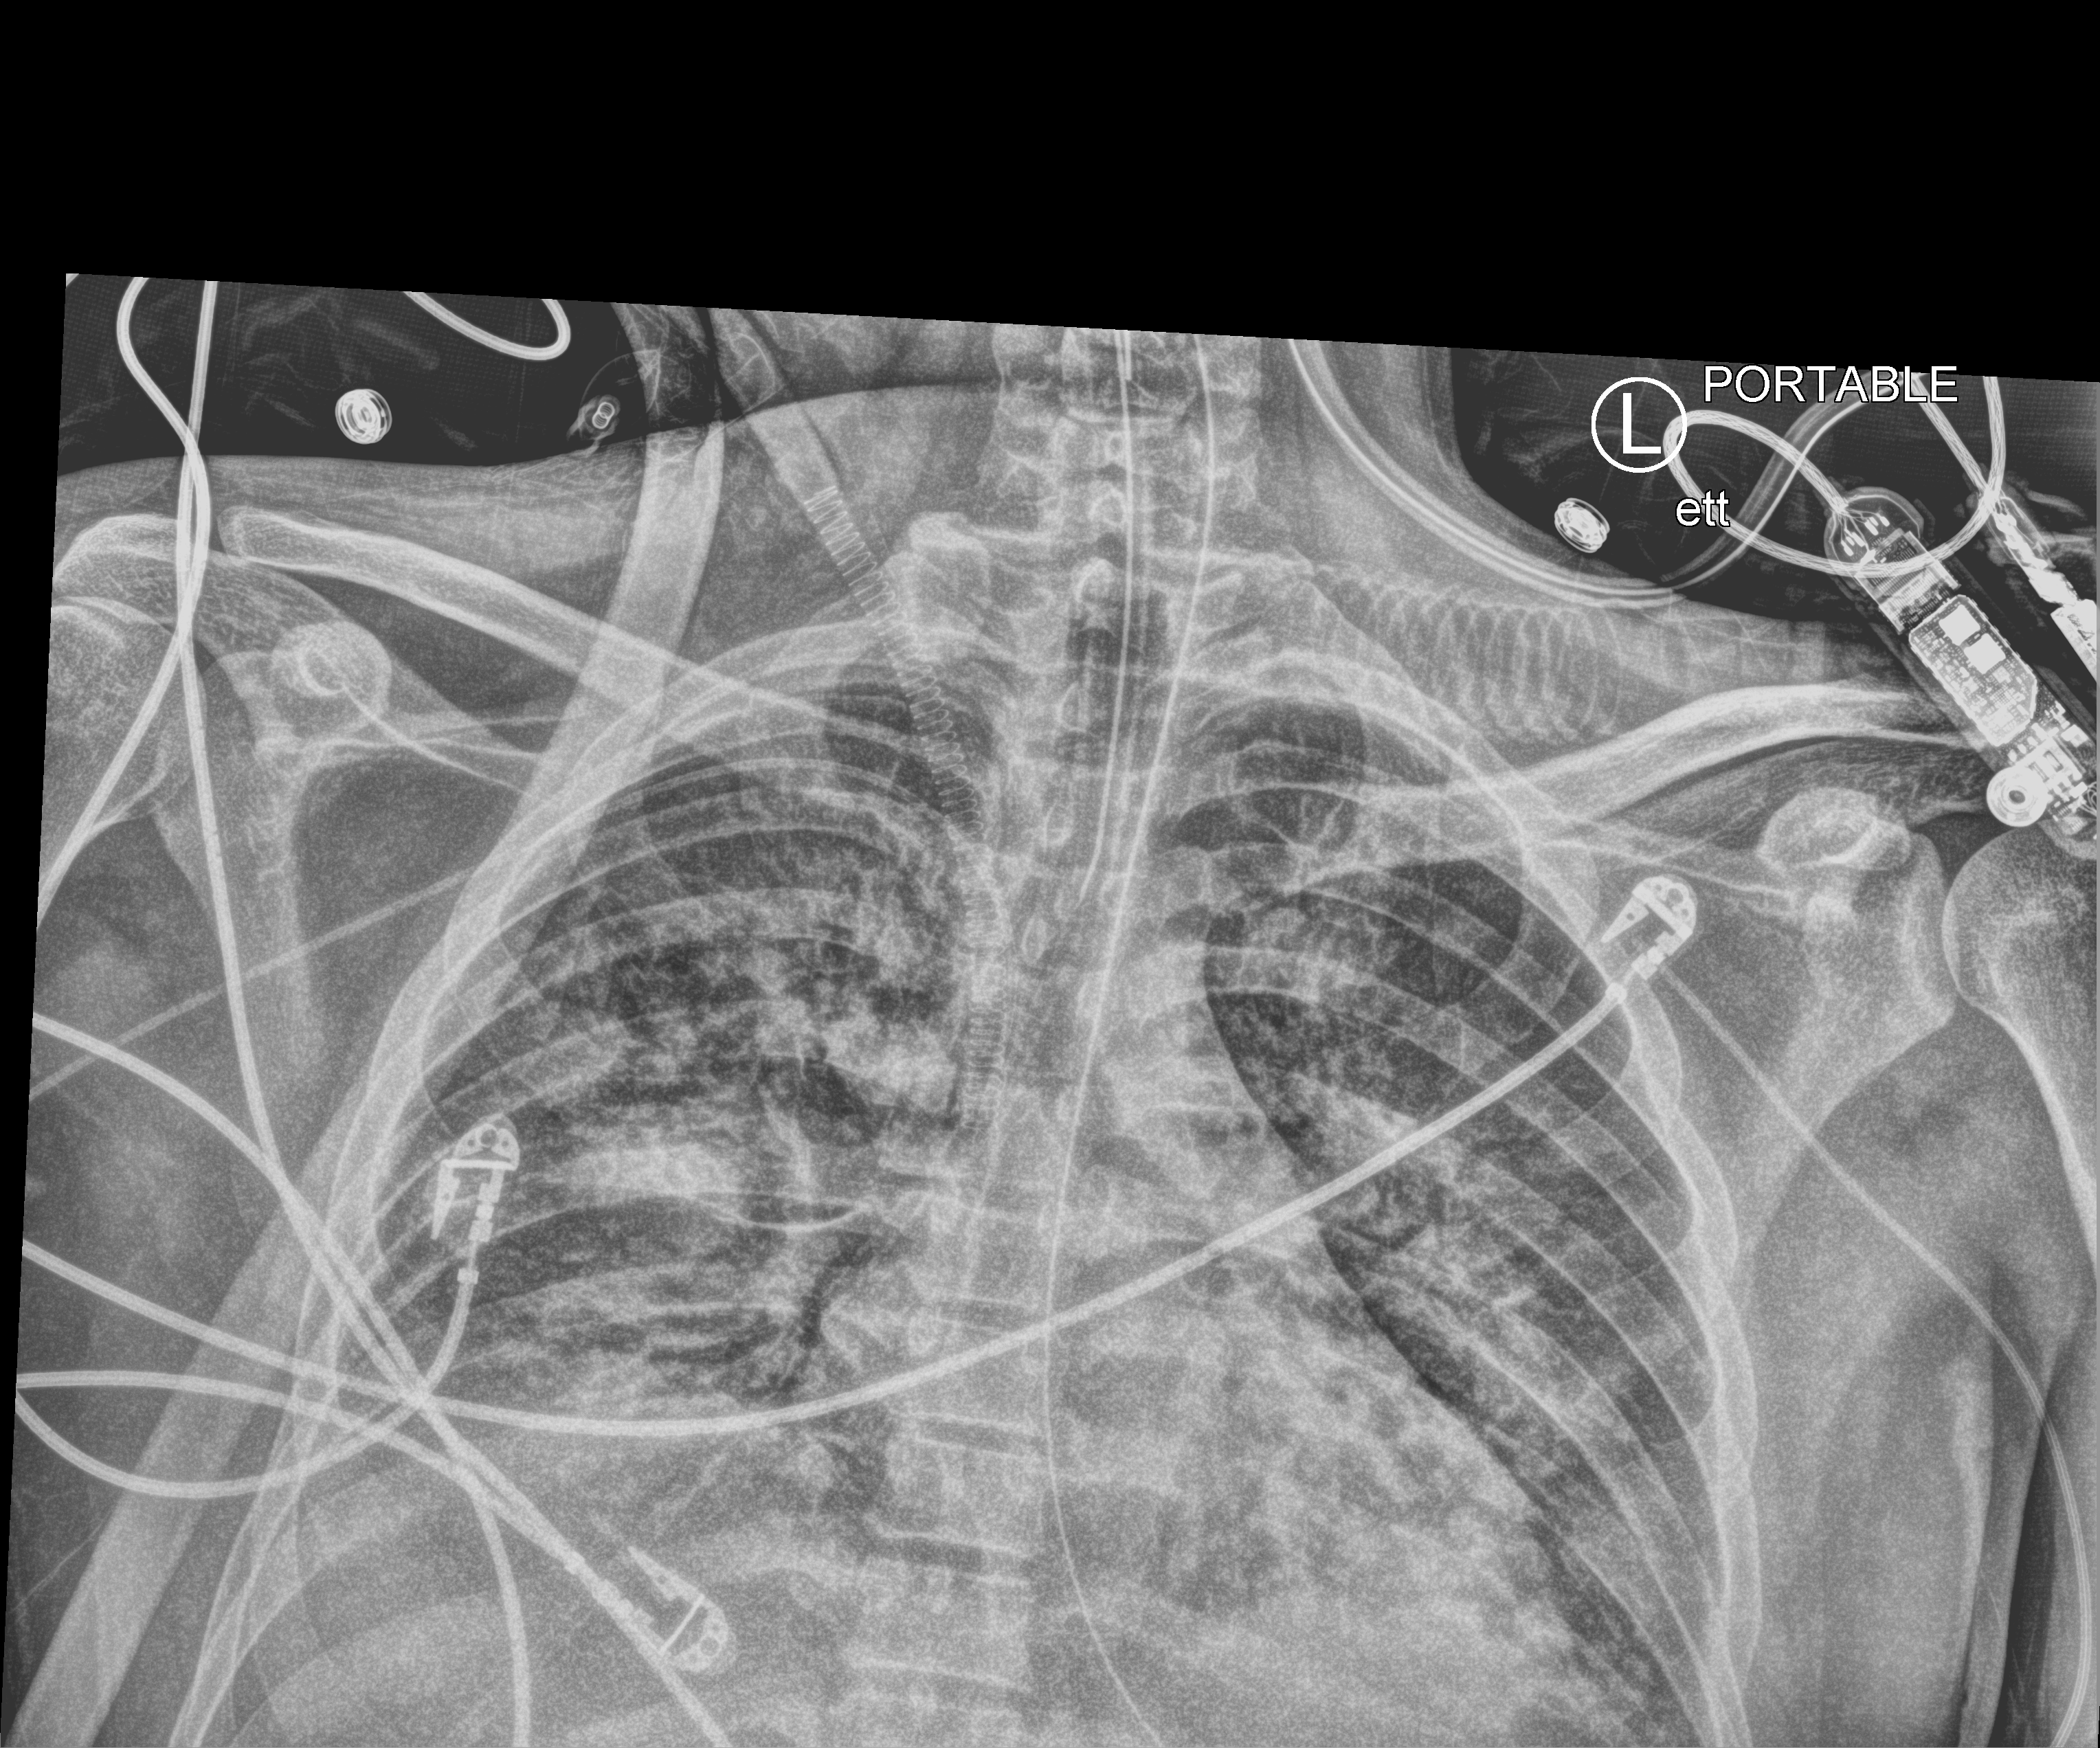
Portable chest radiograph. Adult patient hospitalised with COVID-19, age 18–59 years.
From the hospital-stay record, not from the radiograph (when in the stay this image was taken is not recorded): length of hospital stay: 60 days.